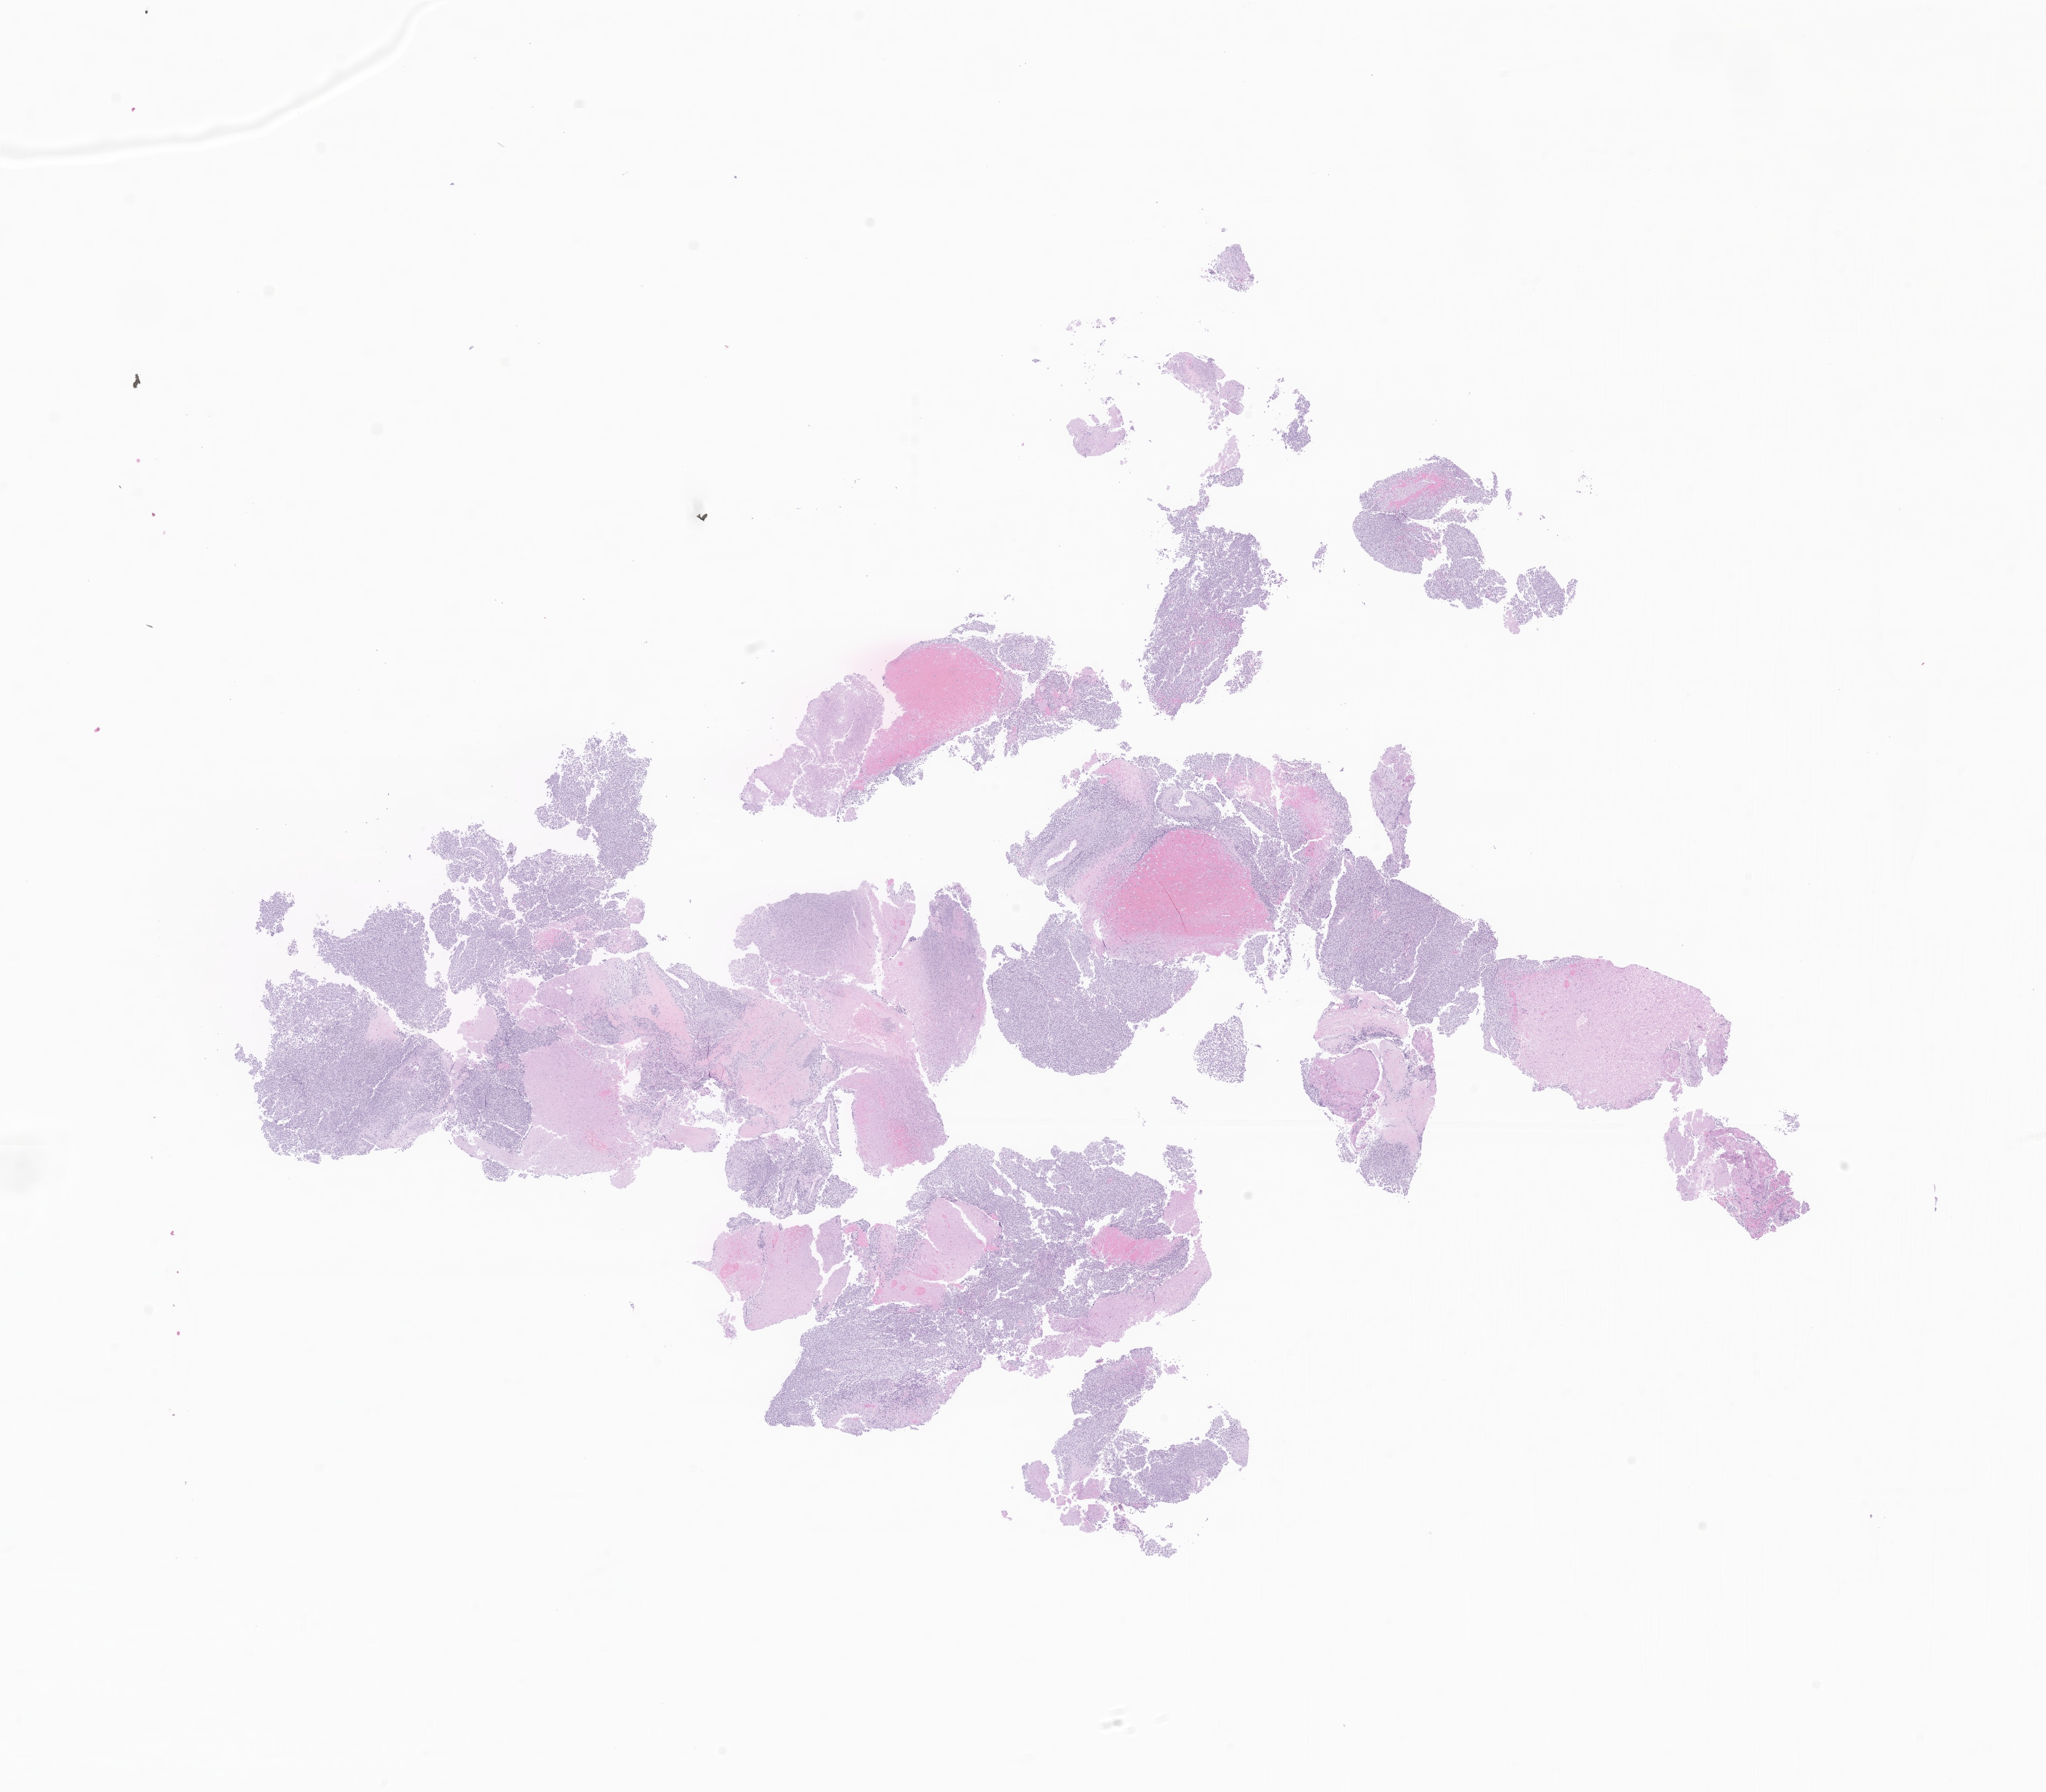
Whole-slide image, H&E stain of tumor tissue from the soft tissue — shown as a low-resolution overview of the whole scanned area (about 16.8 x 14.8 mm). Male patient, age 110 months (9 years 2 months).
• specimen: FFPE section